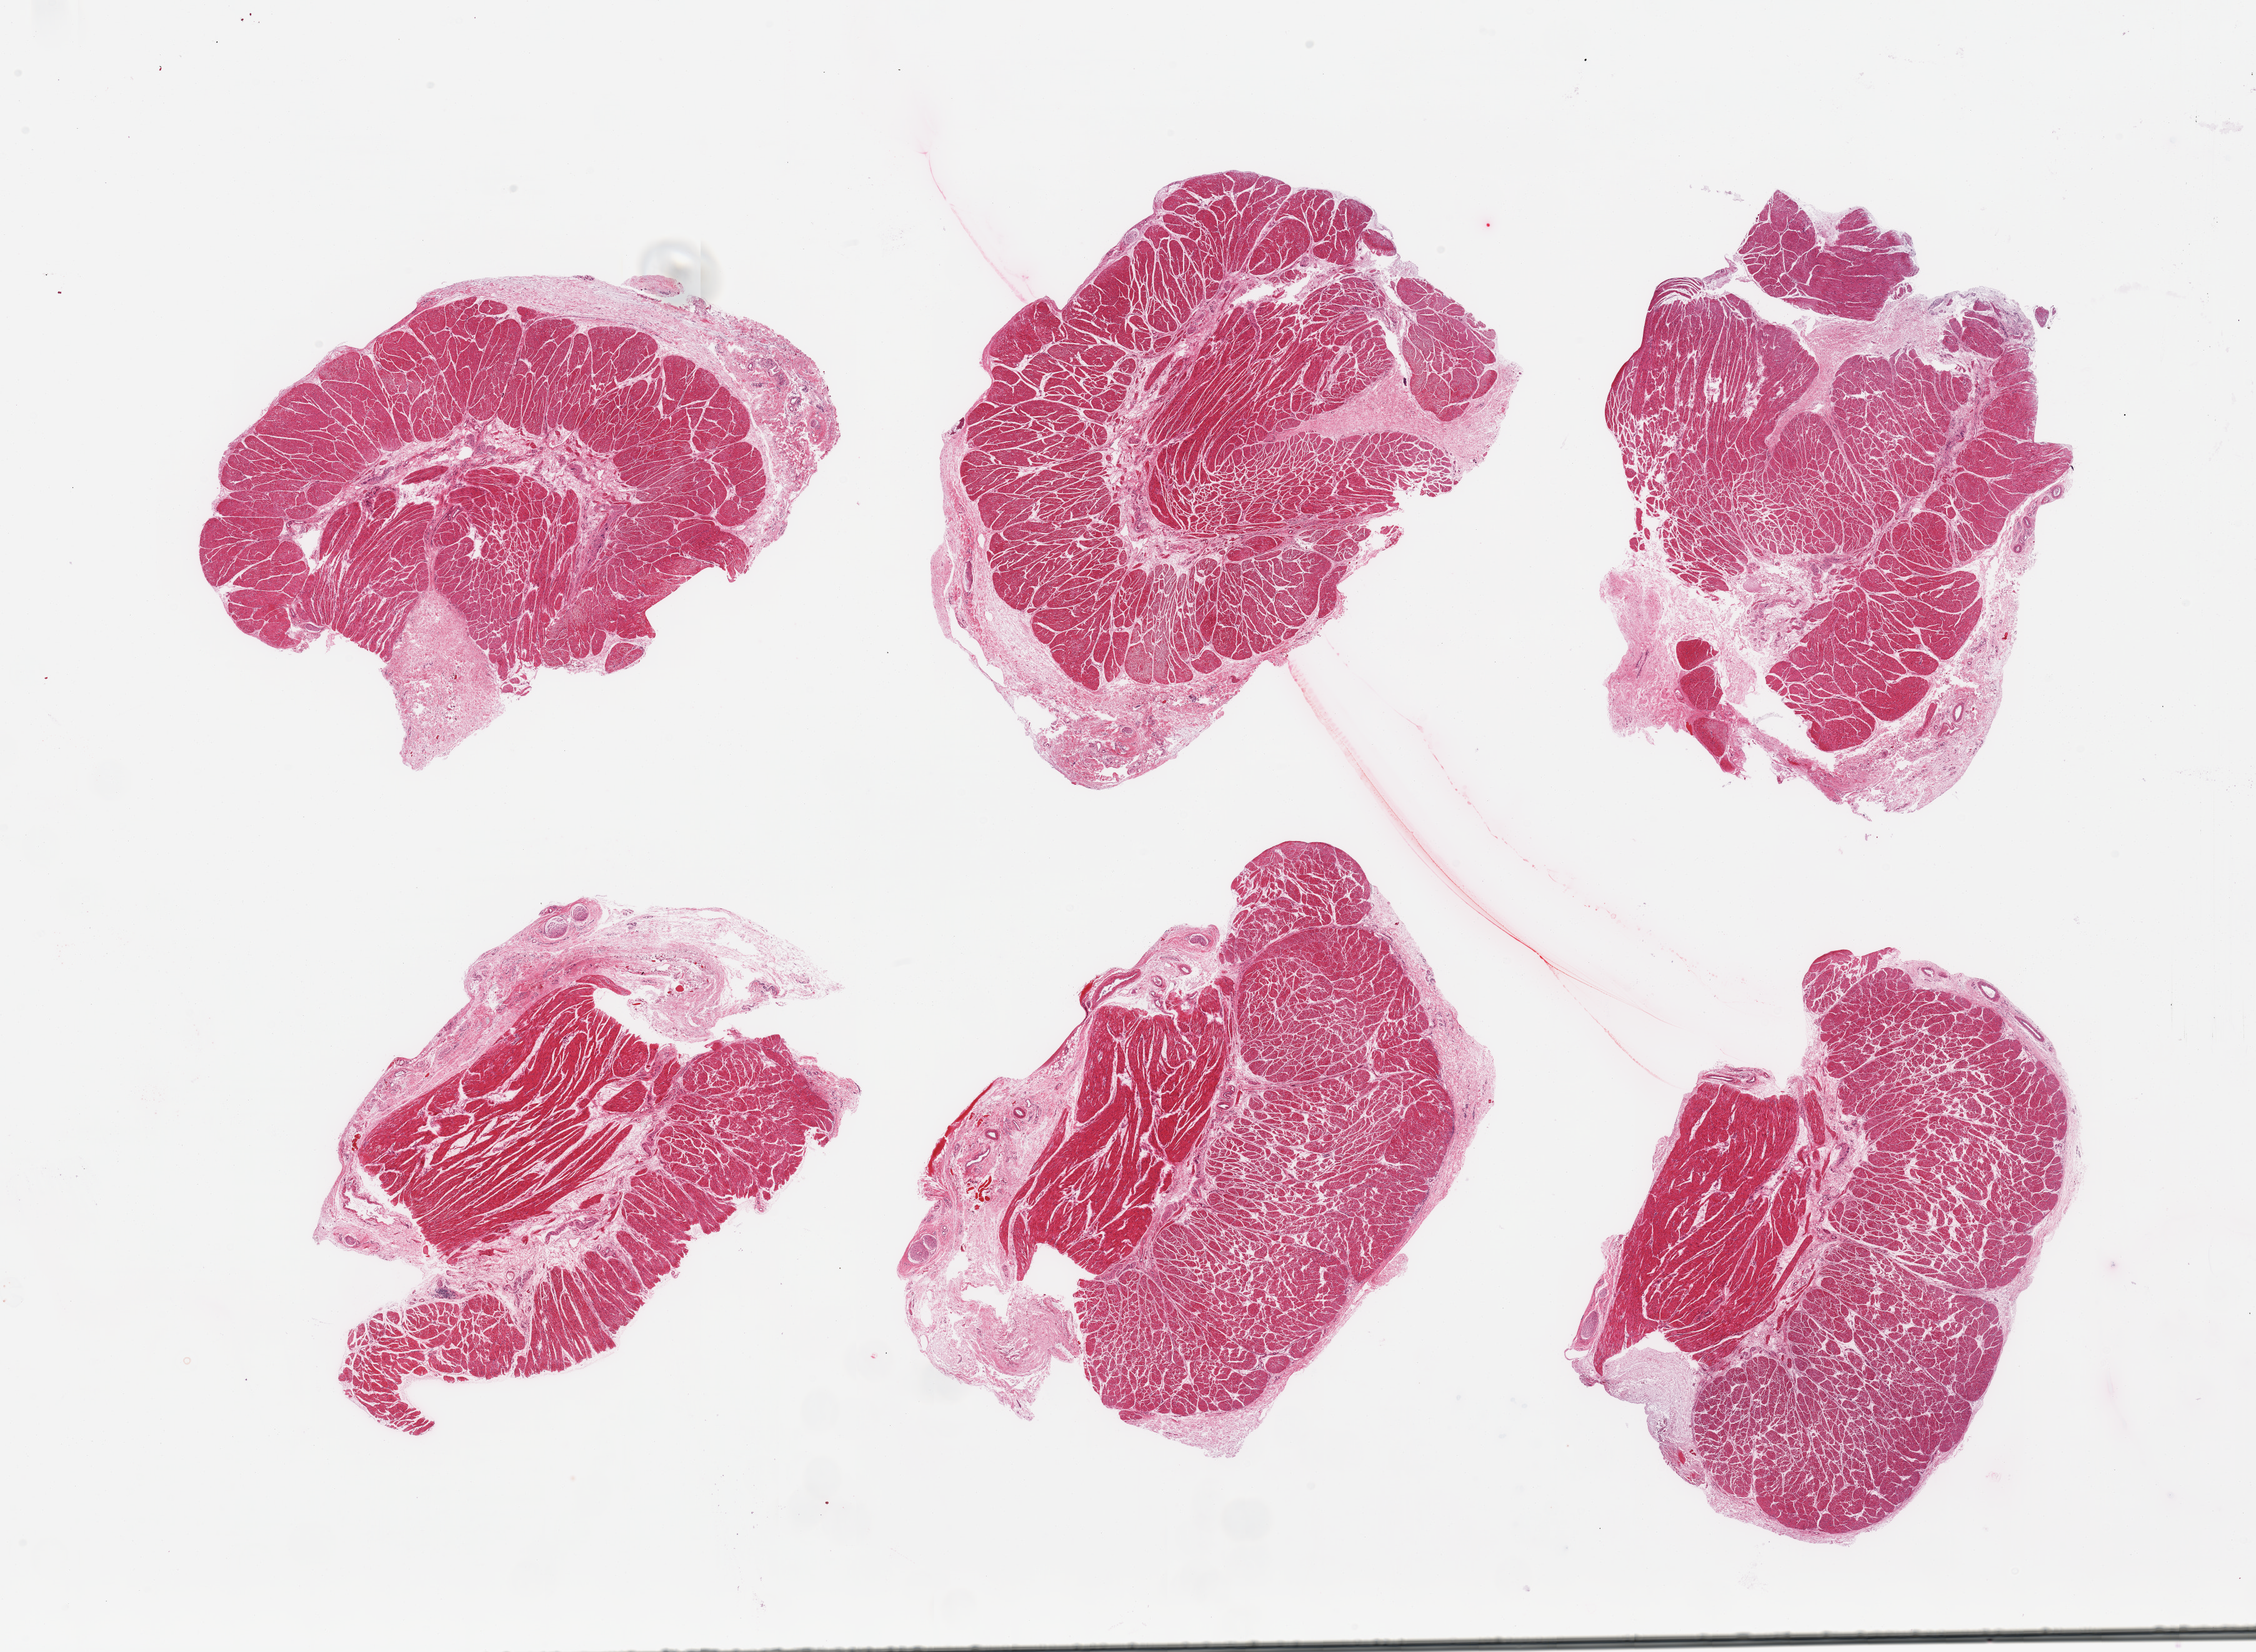
Haematoxylin and eosin whole-slide image, low-resolution overview of the scanned area, about 28.5 x 20.9 mm, PAXgene-fixed, paraffin-embedded tissue, sampled site (target tissue): esophageal muscle, donor tissue sample.
Review note (as recorded): 6 pieces, confirmed target muscularis; adherent rims of serosa up to ~1mm.